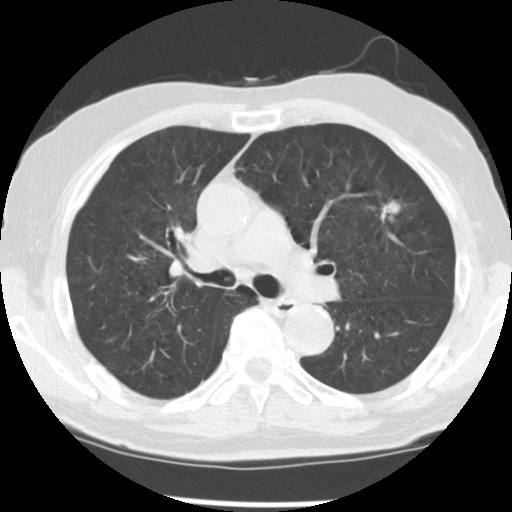
Low-dose screening chest CT, one axial slice; position 80 of 131 along the scan axis; reconstruction kernel STANDARD; lung window (W 1500 / L -600 HU); 512 × 512 image matrix.
Outlined on this slice (expert manual segmentation):
- lesion 1 (tumor, upper lobe of left lung): bounding box (x1, y1, x2, y2) in pixels: (381, 201, 400, 220)